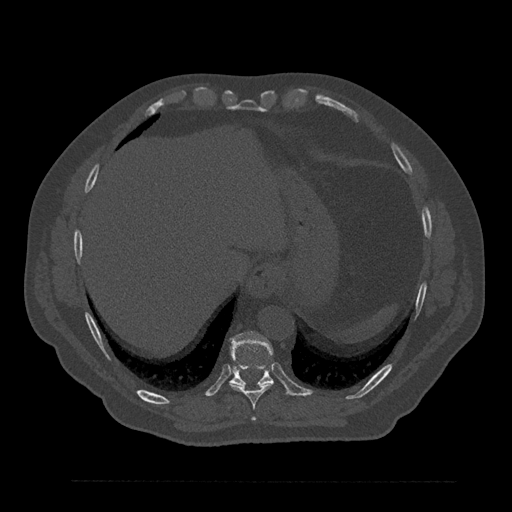
CT including the spine, one axial slice. Slice 382 of 797 in the series (ordered by position). Reconstruction kernel Br40s/3. Bone window (W 1800 / L 400 HU). 0.5 mm slice thickness. 512 × 512 image matrix. Patient: male, 61 years. From the clinical record (not read from this slice): primary cancer: prostate.
Annotated regions visible in this slice (semi-automatically segmented with operator editing):
- T10 vertebra: box from (x=229, y=331) to (x=273, y=386) px
- T8 vertebra: (x=252, y=418)–(x=256, y=421)
- T9 vertebra: (x=230, y=382)–(x=274, y=409)